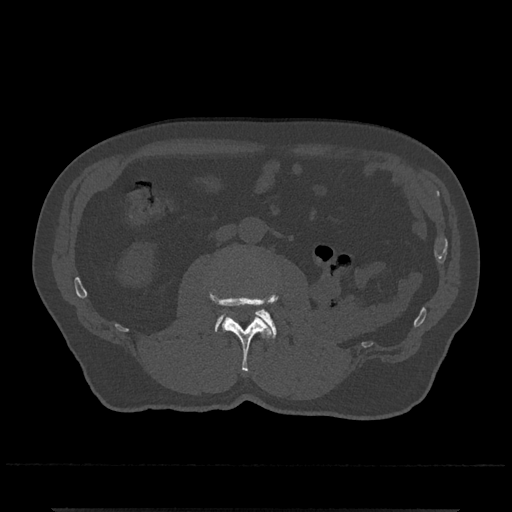
CT including the spine, one axial slice. Slice 269 of 797 in the series (ordered by position). Reconstruction kernel Br40s/3. 120 kVp. Bone window (W 1800 / L 400 HU). 0.5 mm slice thickness. 512 × 512 image matrix, field of view 393 × 393 mm. Male patient, age 67 years. Case-level facts recorded for this patient, not image findings: primary cancer: prostate.
Structures marked on this image (semi-automatically segmented with operator editing):
- L2 vertebra: bounding box [x1, y1, x2, y2] px = [209, 291, 278, 372]
- L3 vertebra: [215, 309, 277, 338]